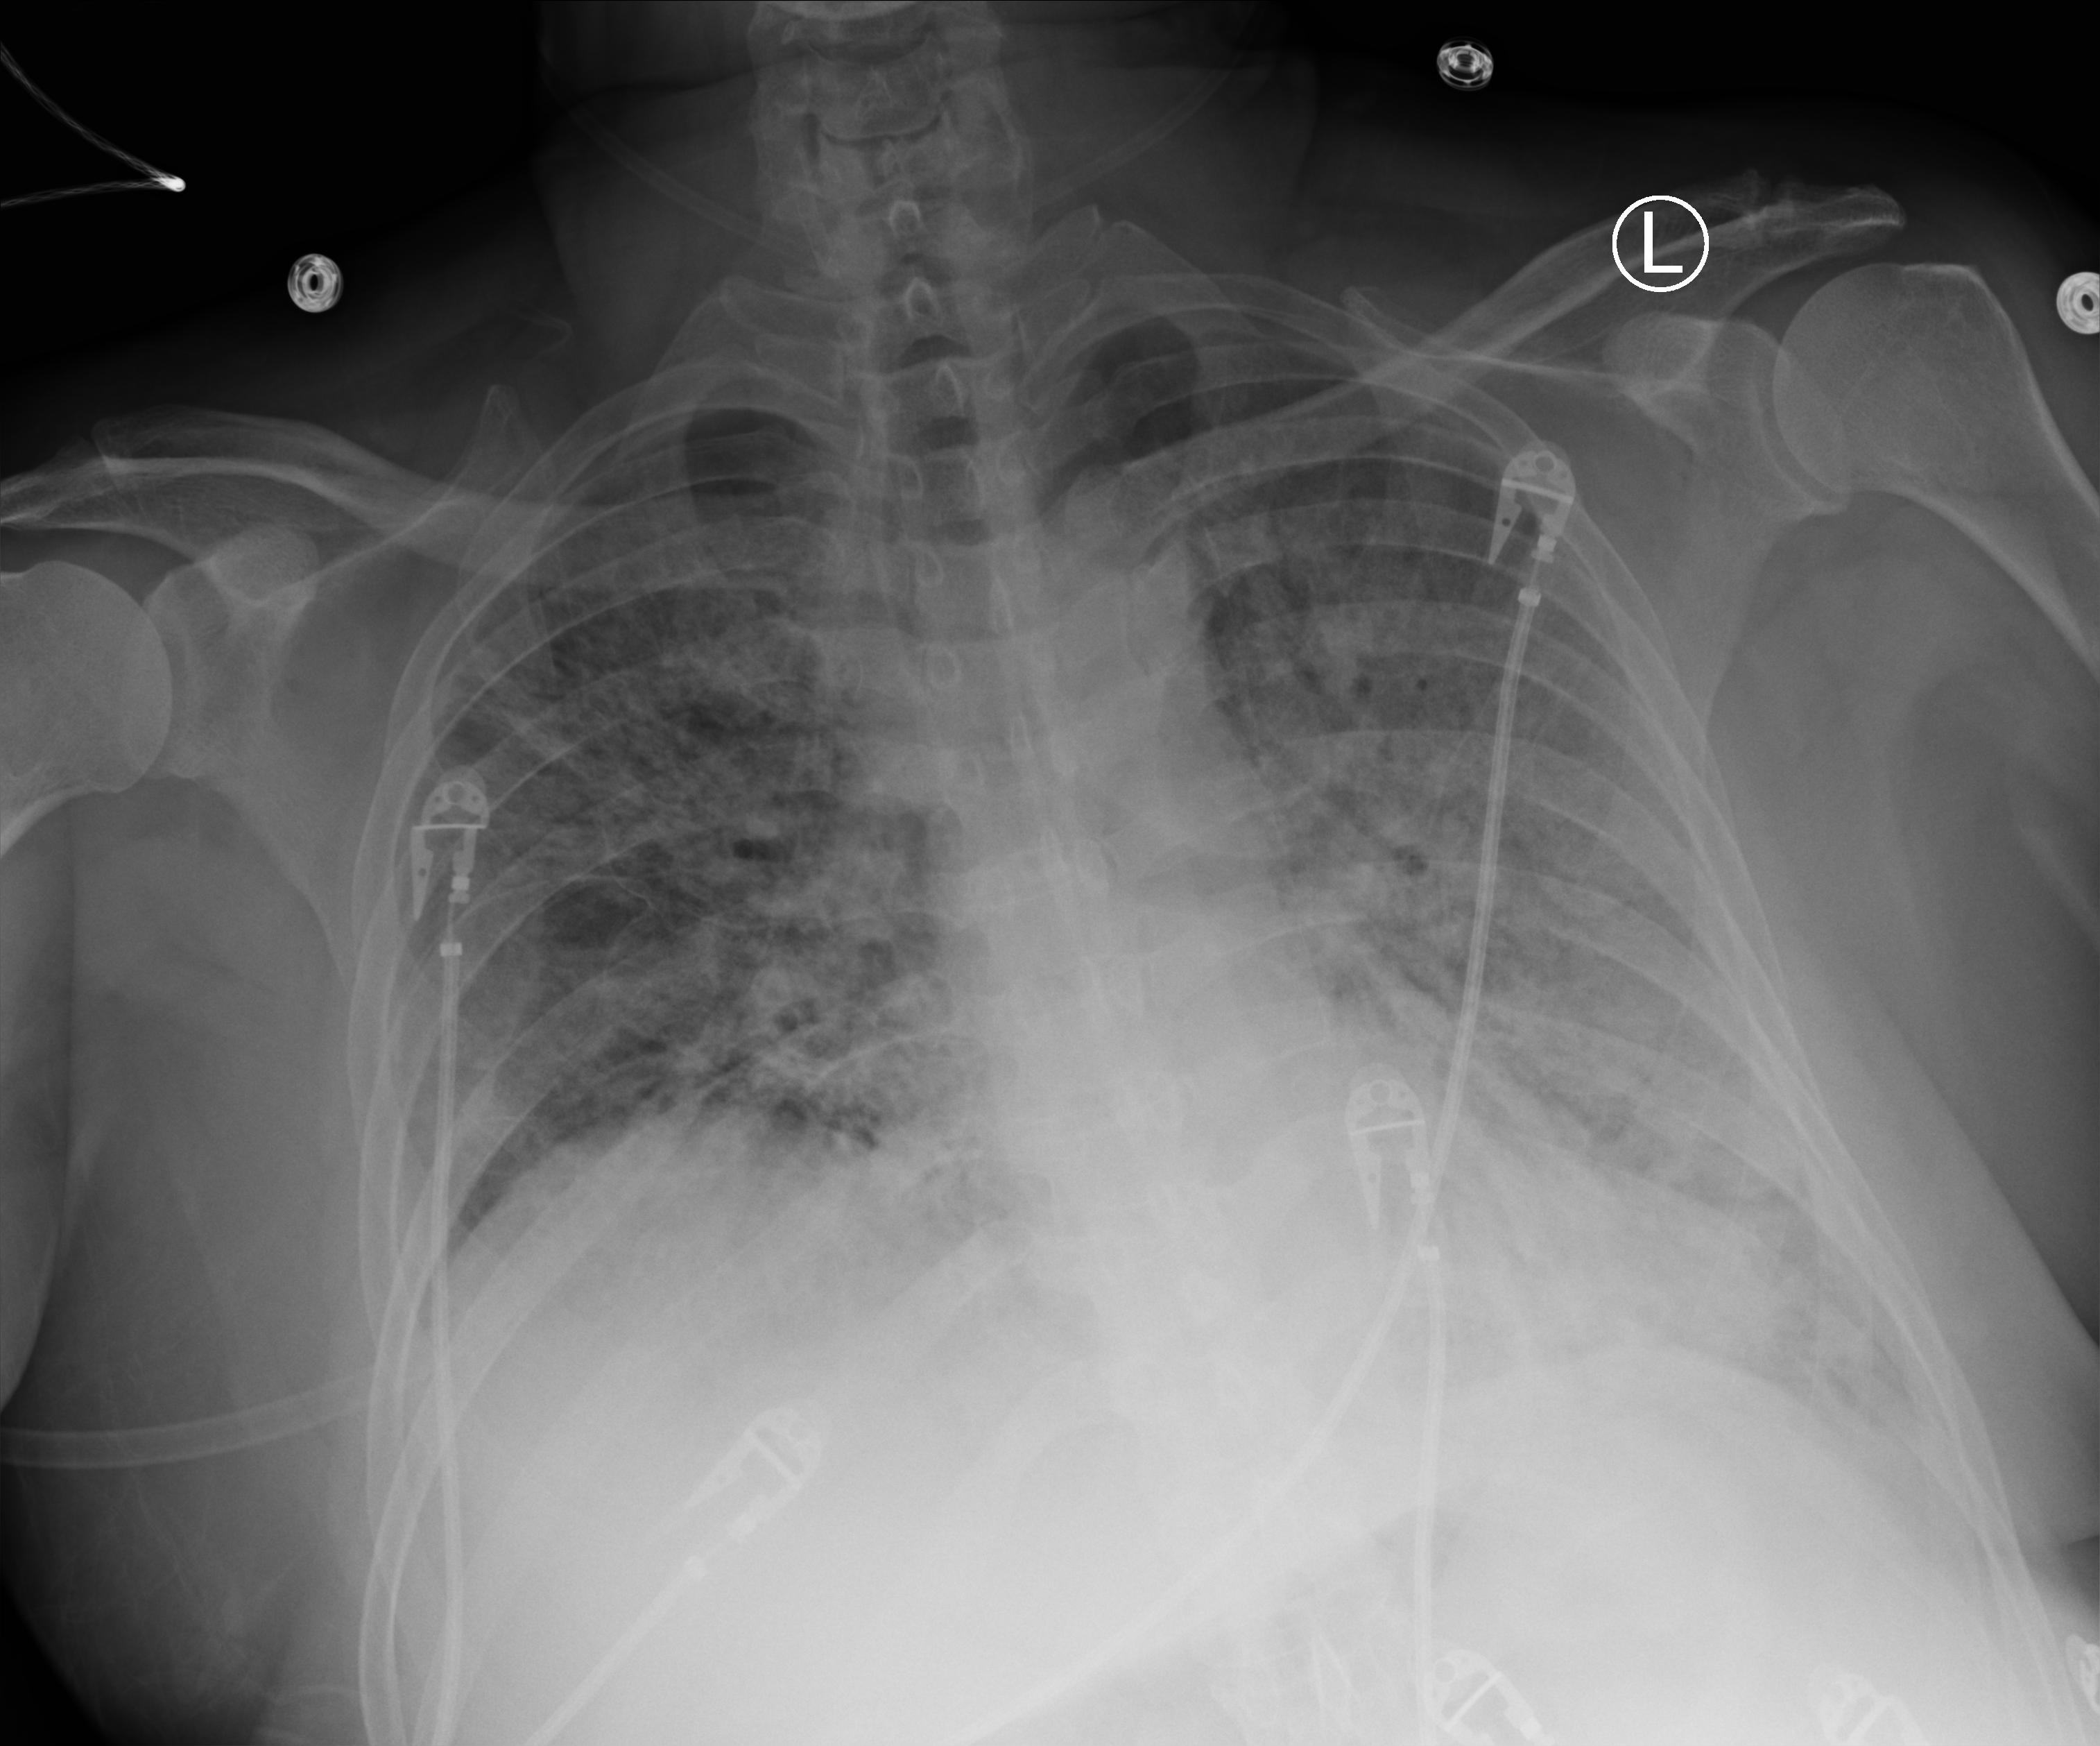
Bedside chest radiograph (computed radiography); anteroposterior (AP) projection. Patient hospitalised with COVID-19; male, aged 18–59 years.
From the hospital-stay record, not from the radiograph (when in the stay this image was taken is not recorded):
- mechanically ventilated during this hospital stay: yes
- chronic kidney disease (admission record): no